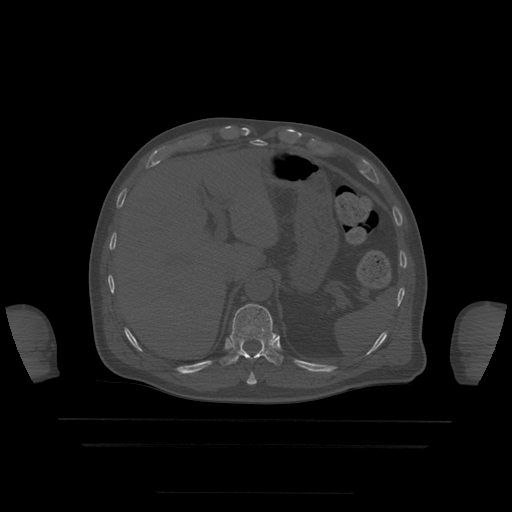
CT including the spine, one axial slice. Slice 224 of 522 in the series (ordered by position). Bone window (W 1800 / L 400 HU). 1.25 mm slice thickness. 512 × 512 image matrix, field of view 436 × 436 mm. Patient age 68 years. From the clinical record (not read from this slice): primary cancer: urothelial.
Outlined on this slice (semi-automatically segmented with operator editing):
- T10 vertebra: bounding box <247,373,257,385> (left, top, right, bottom; pixels)
- T11 vertebra: <221,304,283,366>